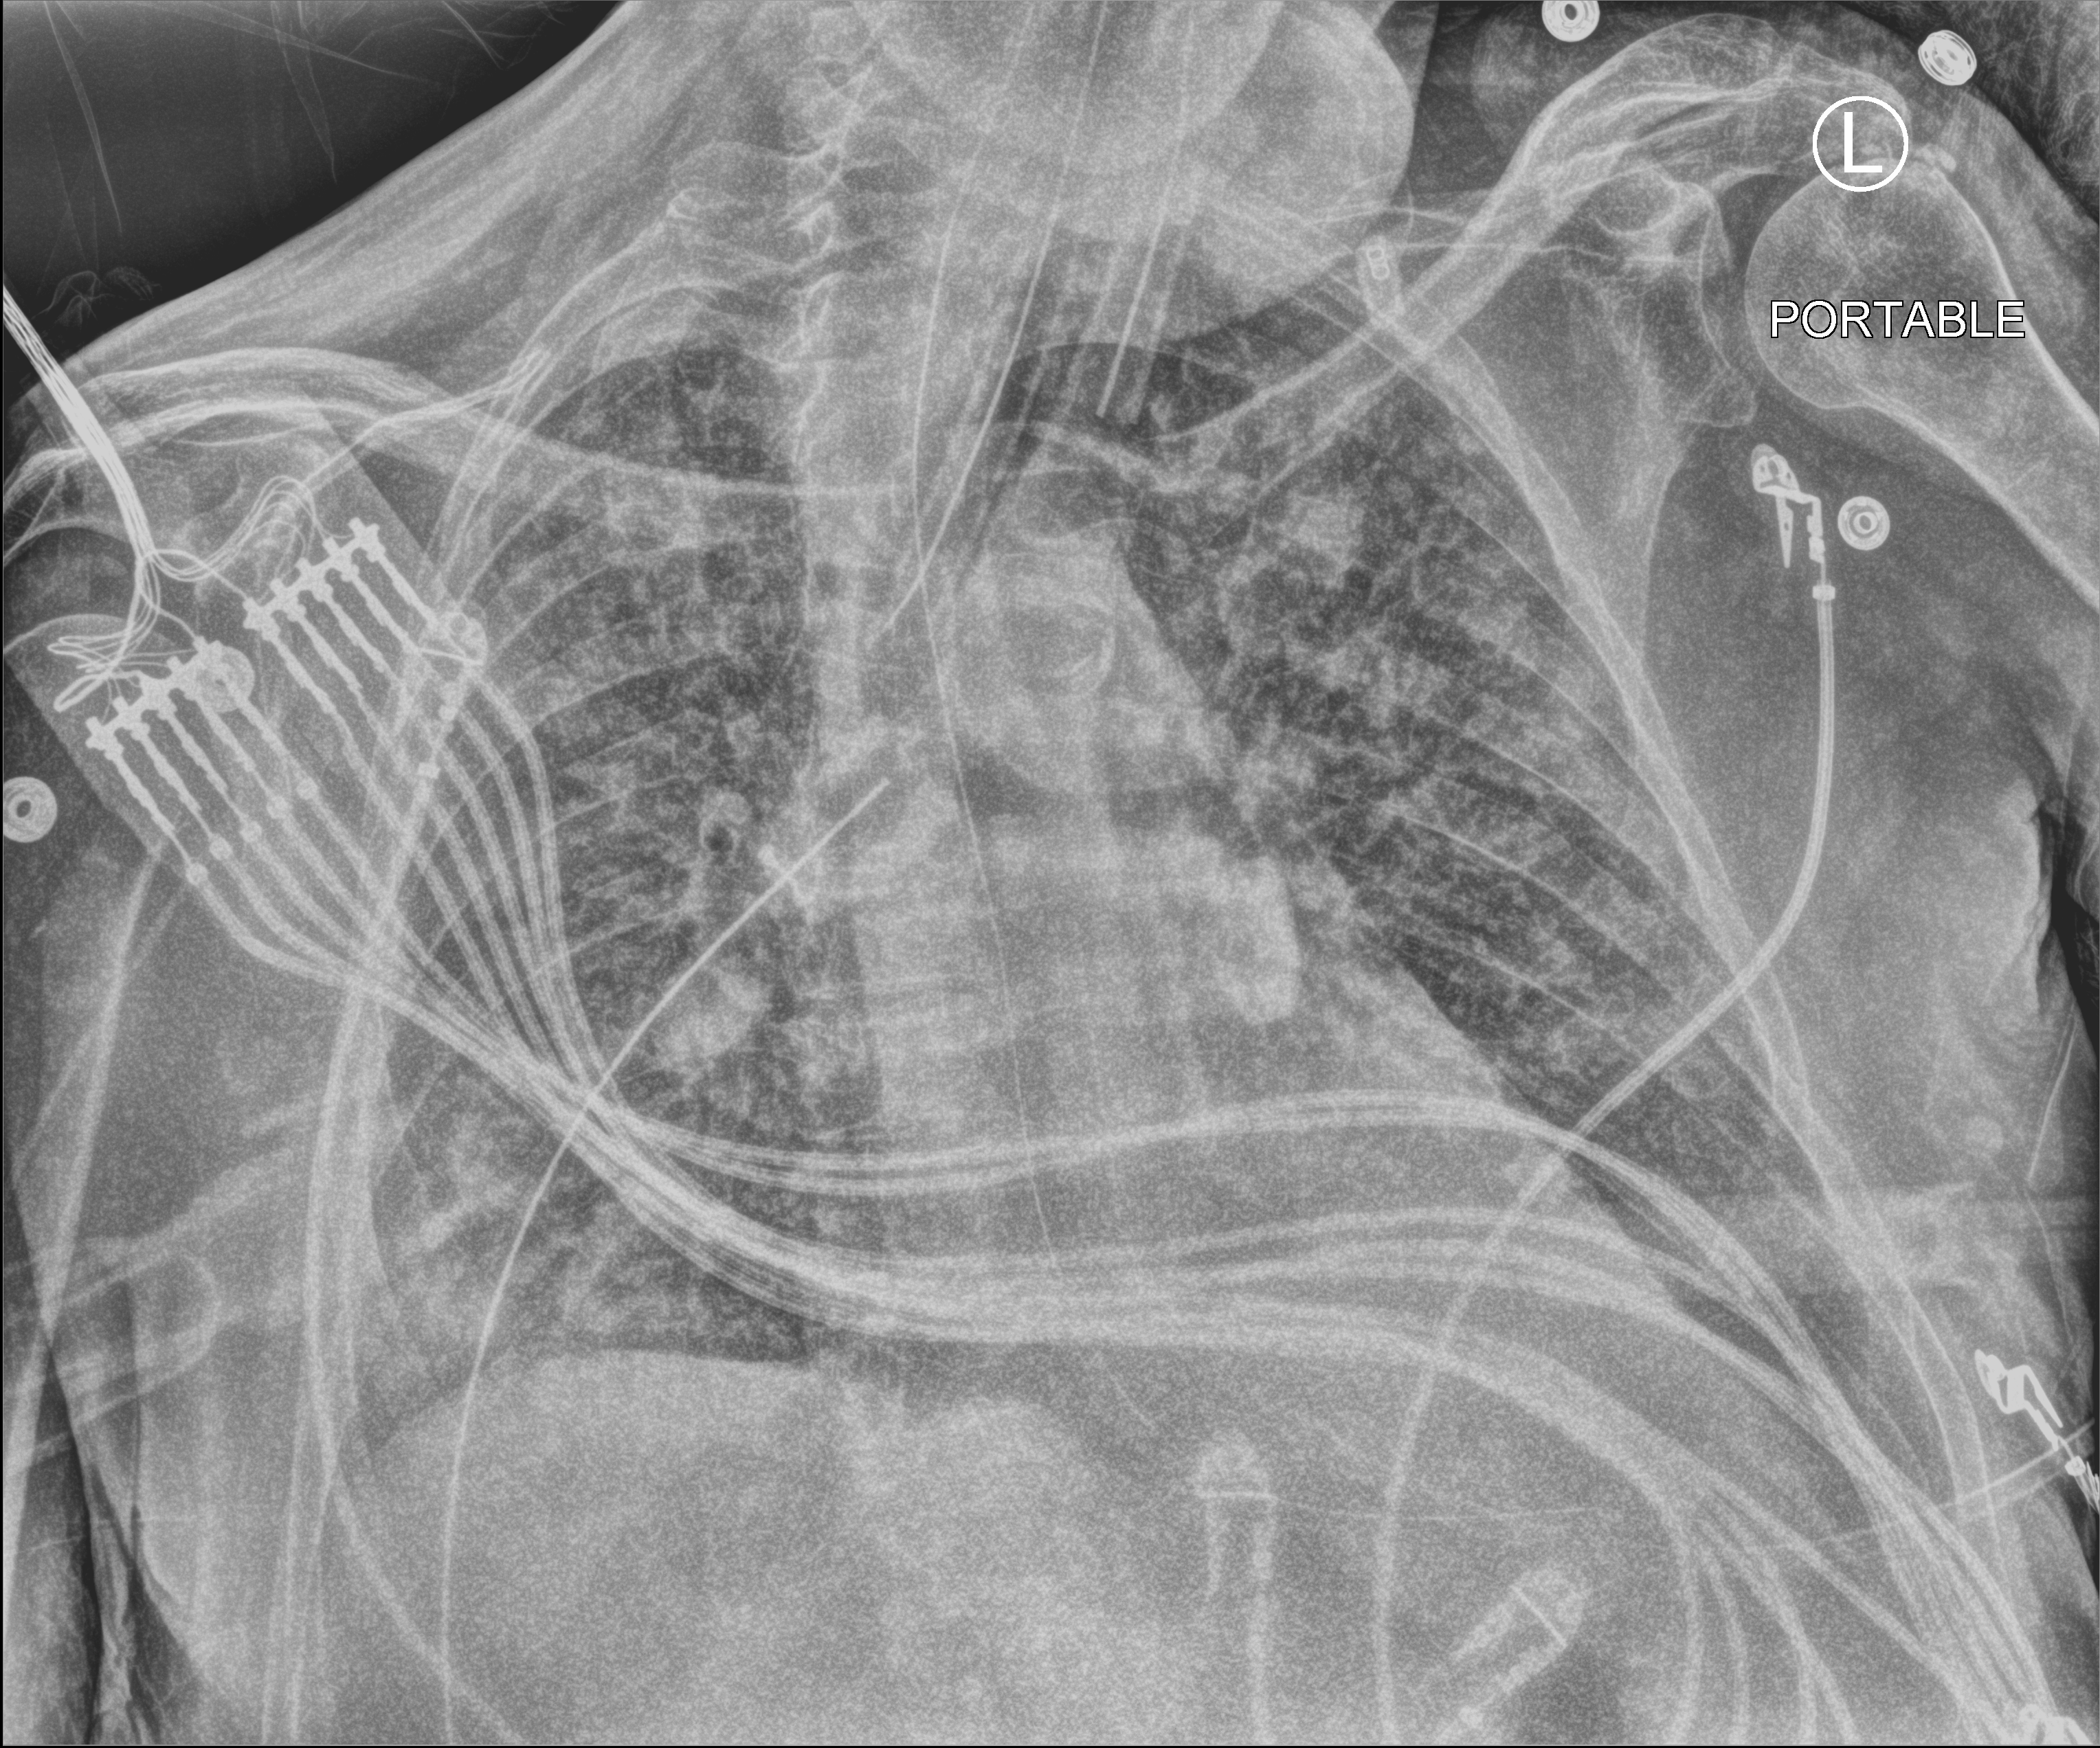
Bedside chest radiograph (computed radiography), anteroposterior (AP) projection. Patient hospitalised with COVID-19; male, aged 60–74 years.
Admission-level facts for this patient (not findings on this image; timing relative to this image not recorded):
- mechanically ventilated during this hospital stay: yes